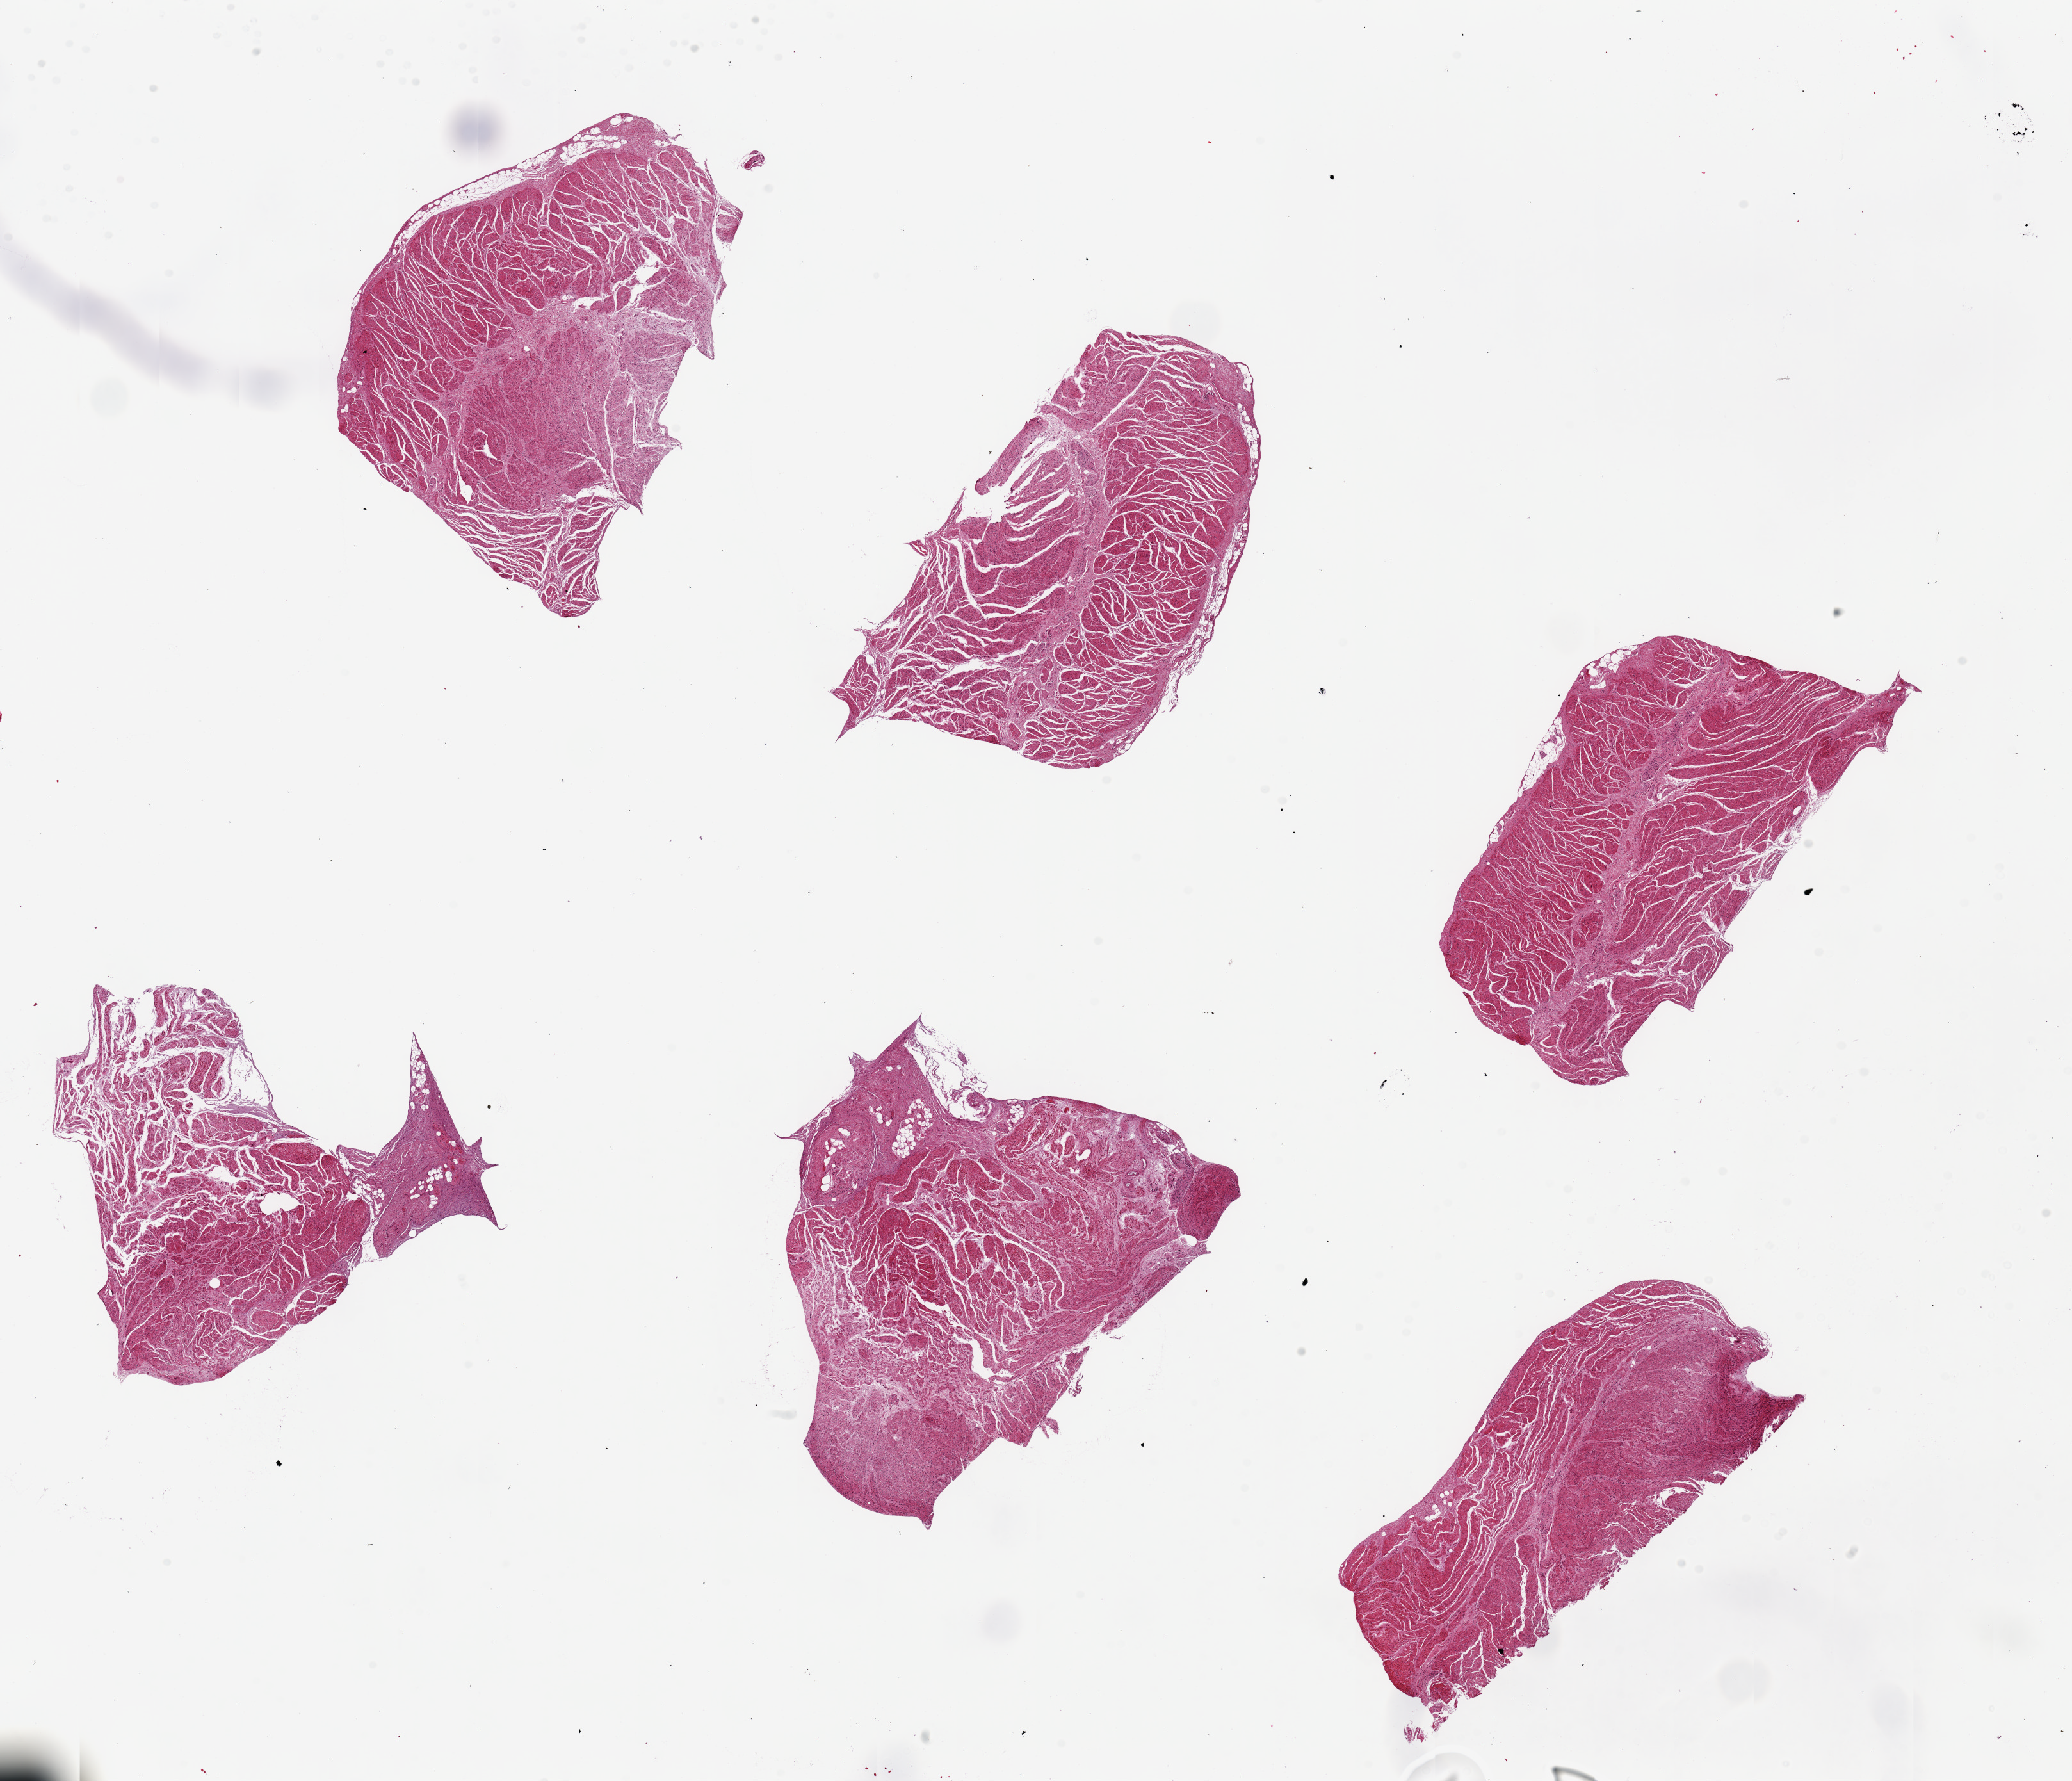
Digitized hematoxylin and eosin (H&E)-stained section, brightfield — shown as a low-resolution overview of the whole scanned area (about 25.6 x 22.0 mm); PAXgene-fixed paraffin-embedded (PFPE) section; section of gastroesophageal junction (target tissue); tissue donor sample. Donor: male.
- review note (as recorded): 6 pieces, up to 7x3mm; all muscle, no mucosa (good!)